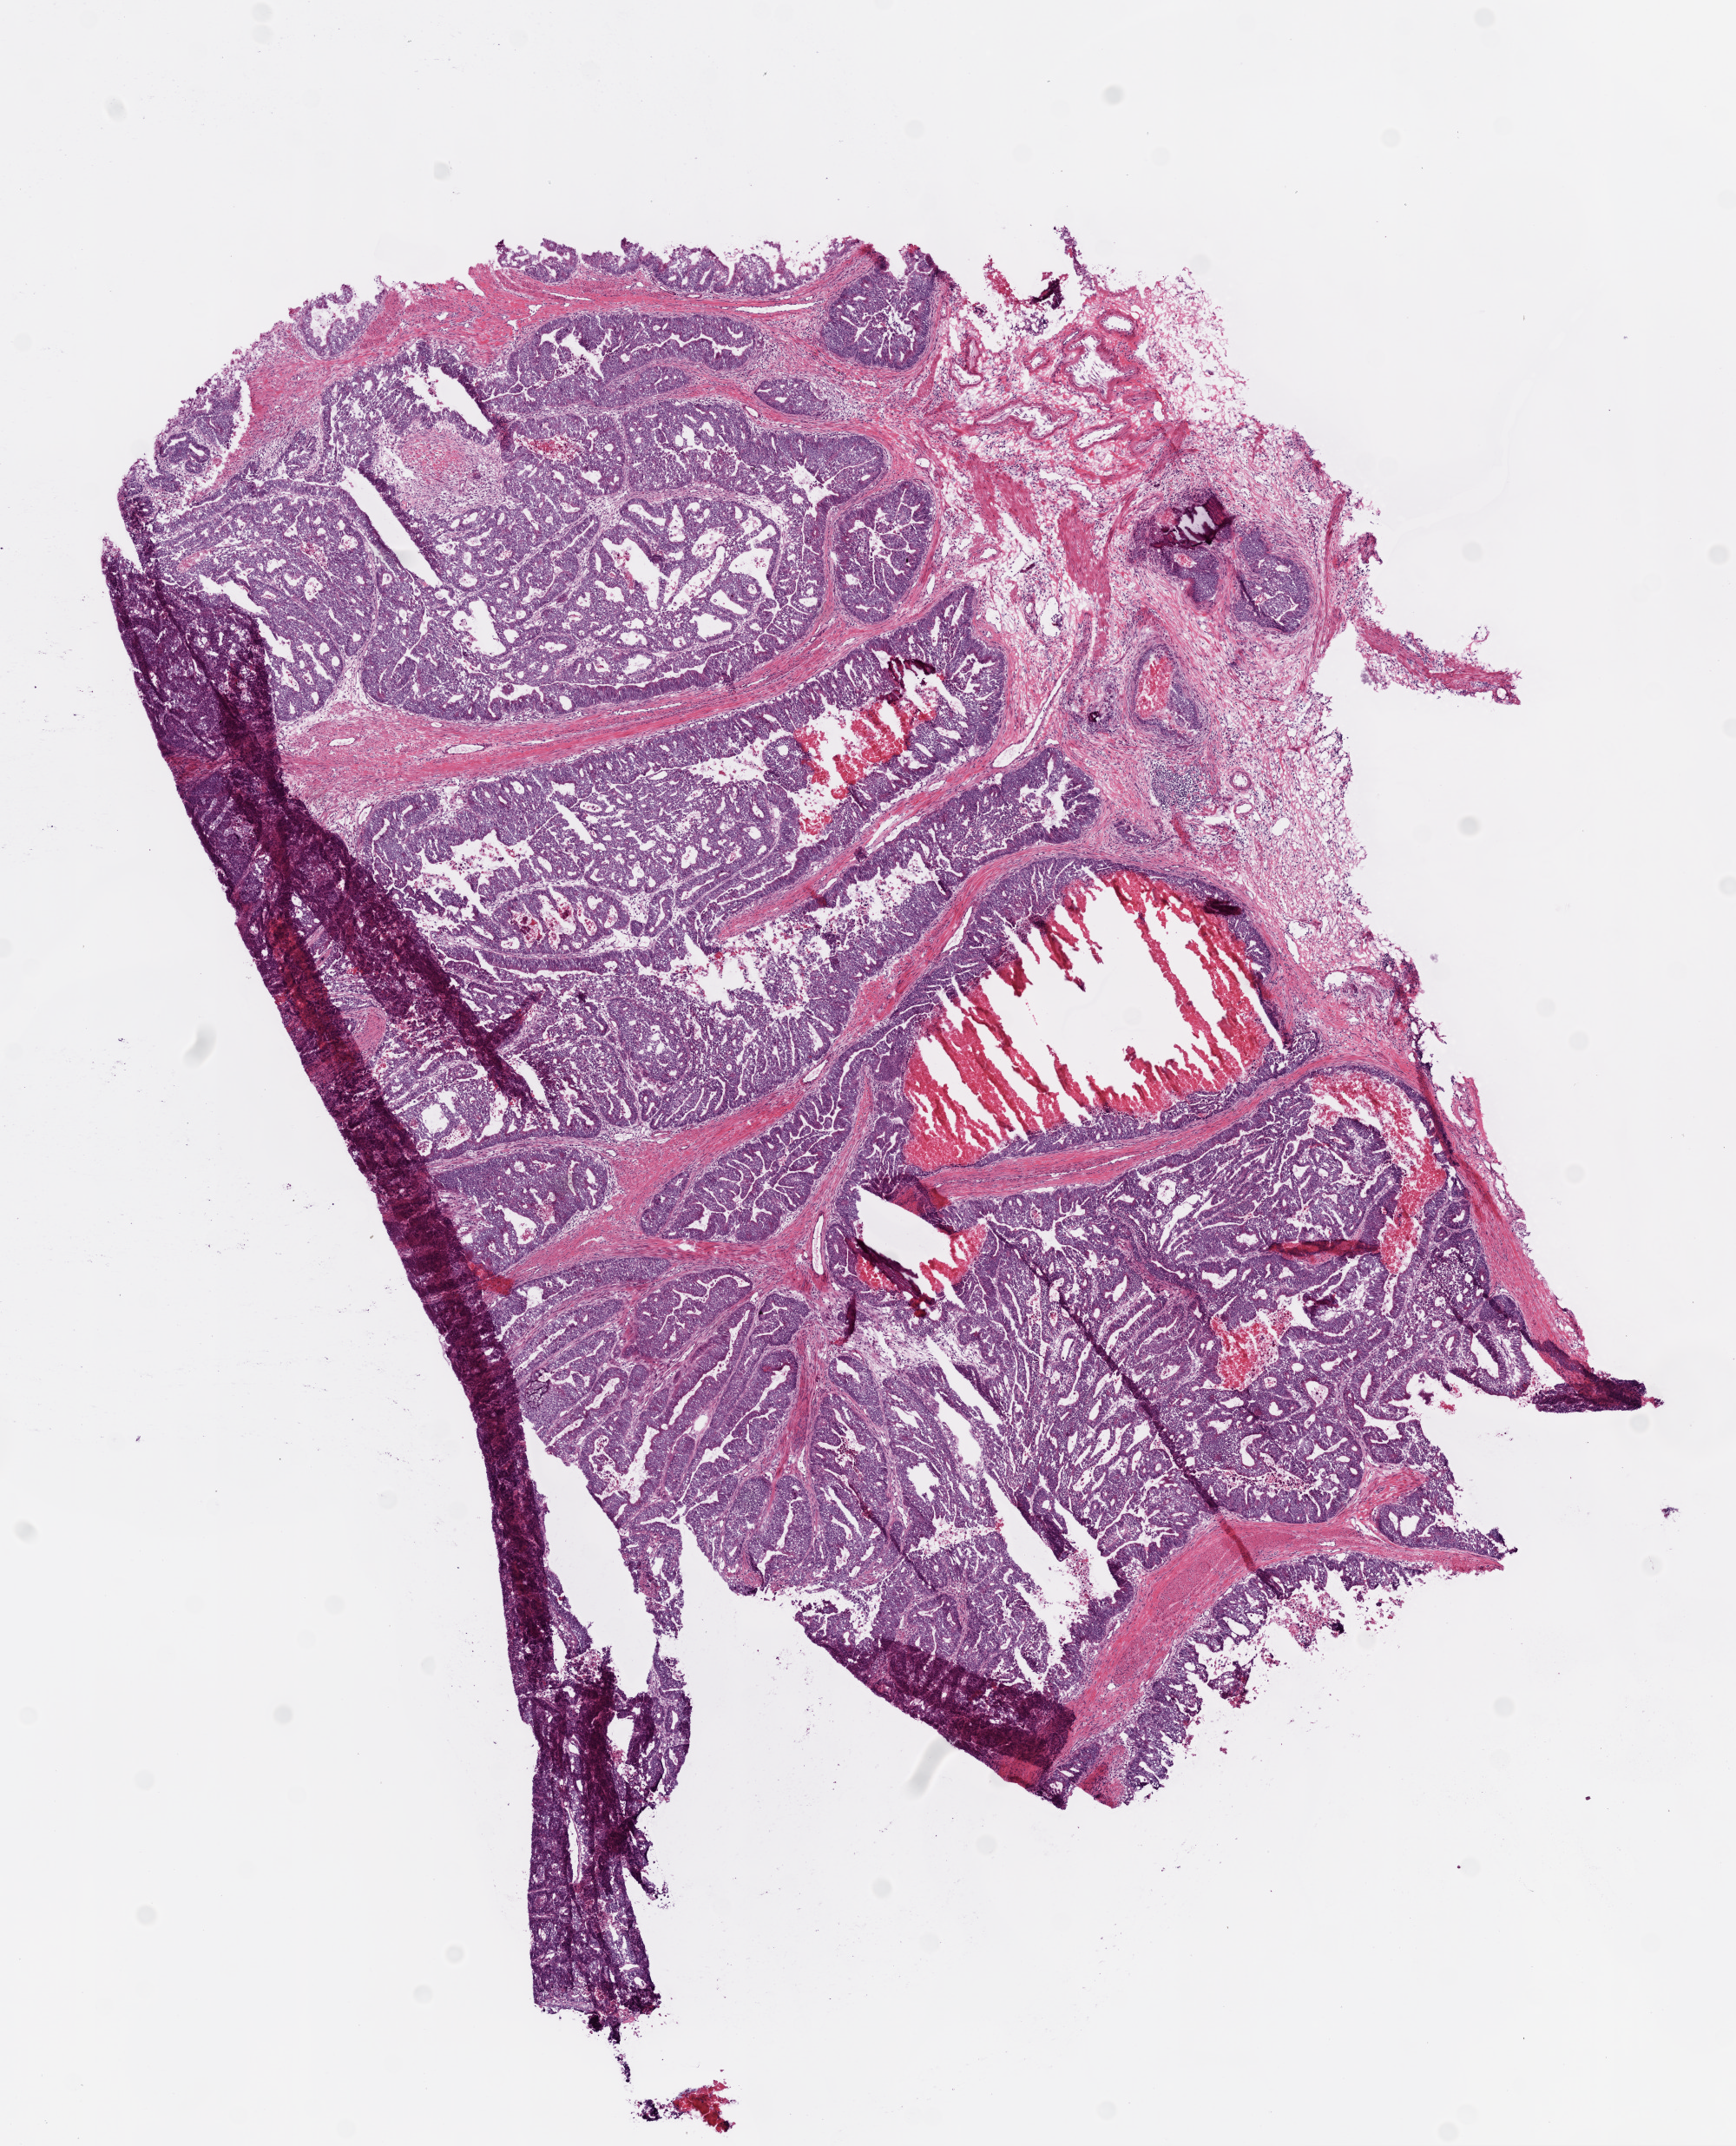
H&E whole-slide image — whole scanned area (about 8.0 x 9.9 mm, acquisition: 20x scan) shown as a low-resolution overview. Frozen section. Colon, primary tumour sample. Female, age 68 years at initial diagnosis. Composition of this section per pathologist review: tumour cells 80%, tumour nuclei 90%, normal cells 5%, stromal cells 5%, necrosis 10%.
* AJCC pathologic stage: IIIC
* histologic diagnosis: Adenocarcinoma, NOS
* lymph nodes positive (case pathology): 5 of 30 examined